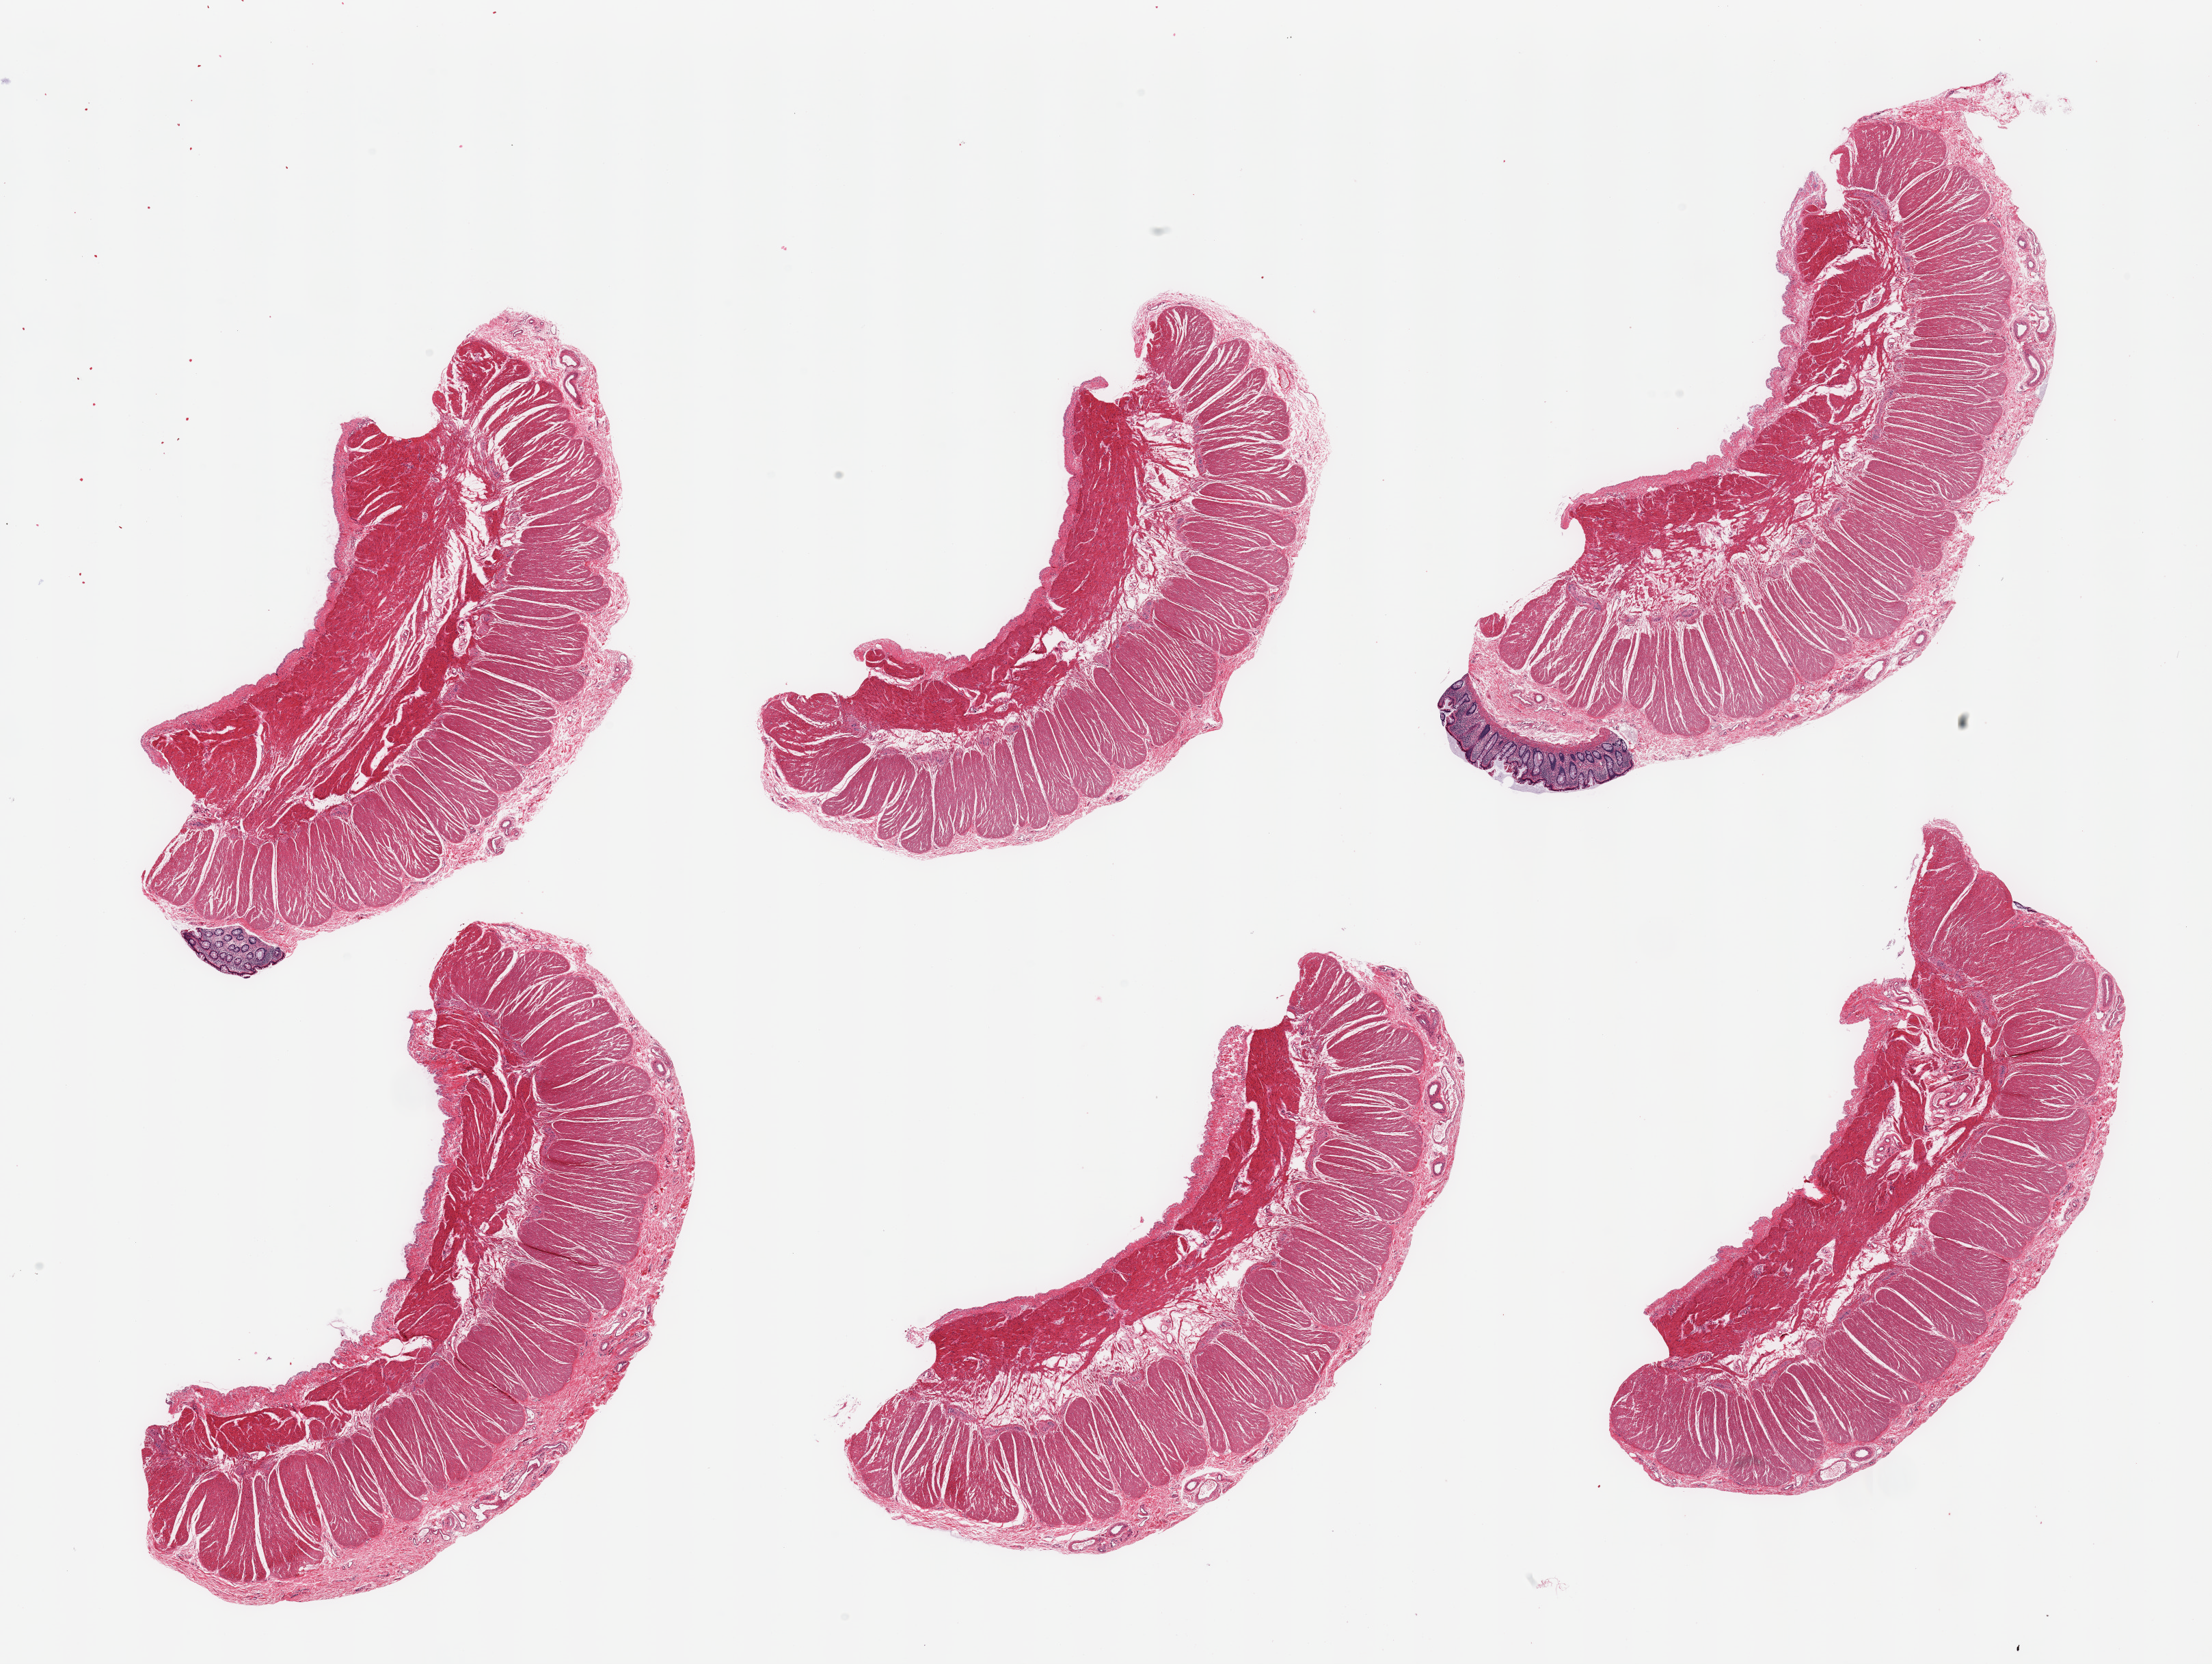
Hematoxylin and eosin (H&E) whole-slide image, brightfield — shown as a low-resolution overview of the whole scanned area (about 25.6 x 19.3 mm). PAXgene-fixed paraffin-embedded (PFPE) section. Section of sigmoid colon (target tissue). Tissue donor sample. Female donor.
• review note (as recorded): 6 pieces; target muscularis with two small strips of residual mucosa